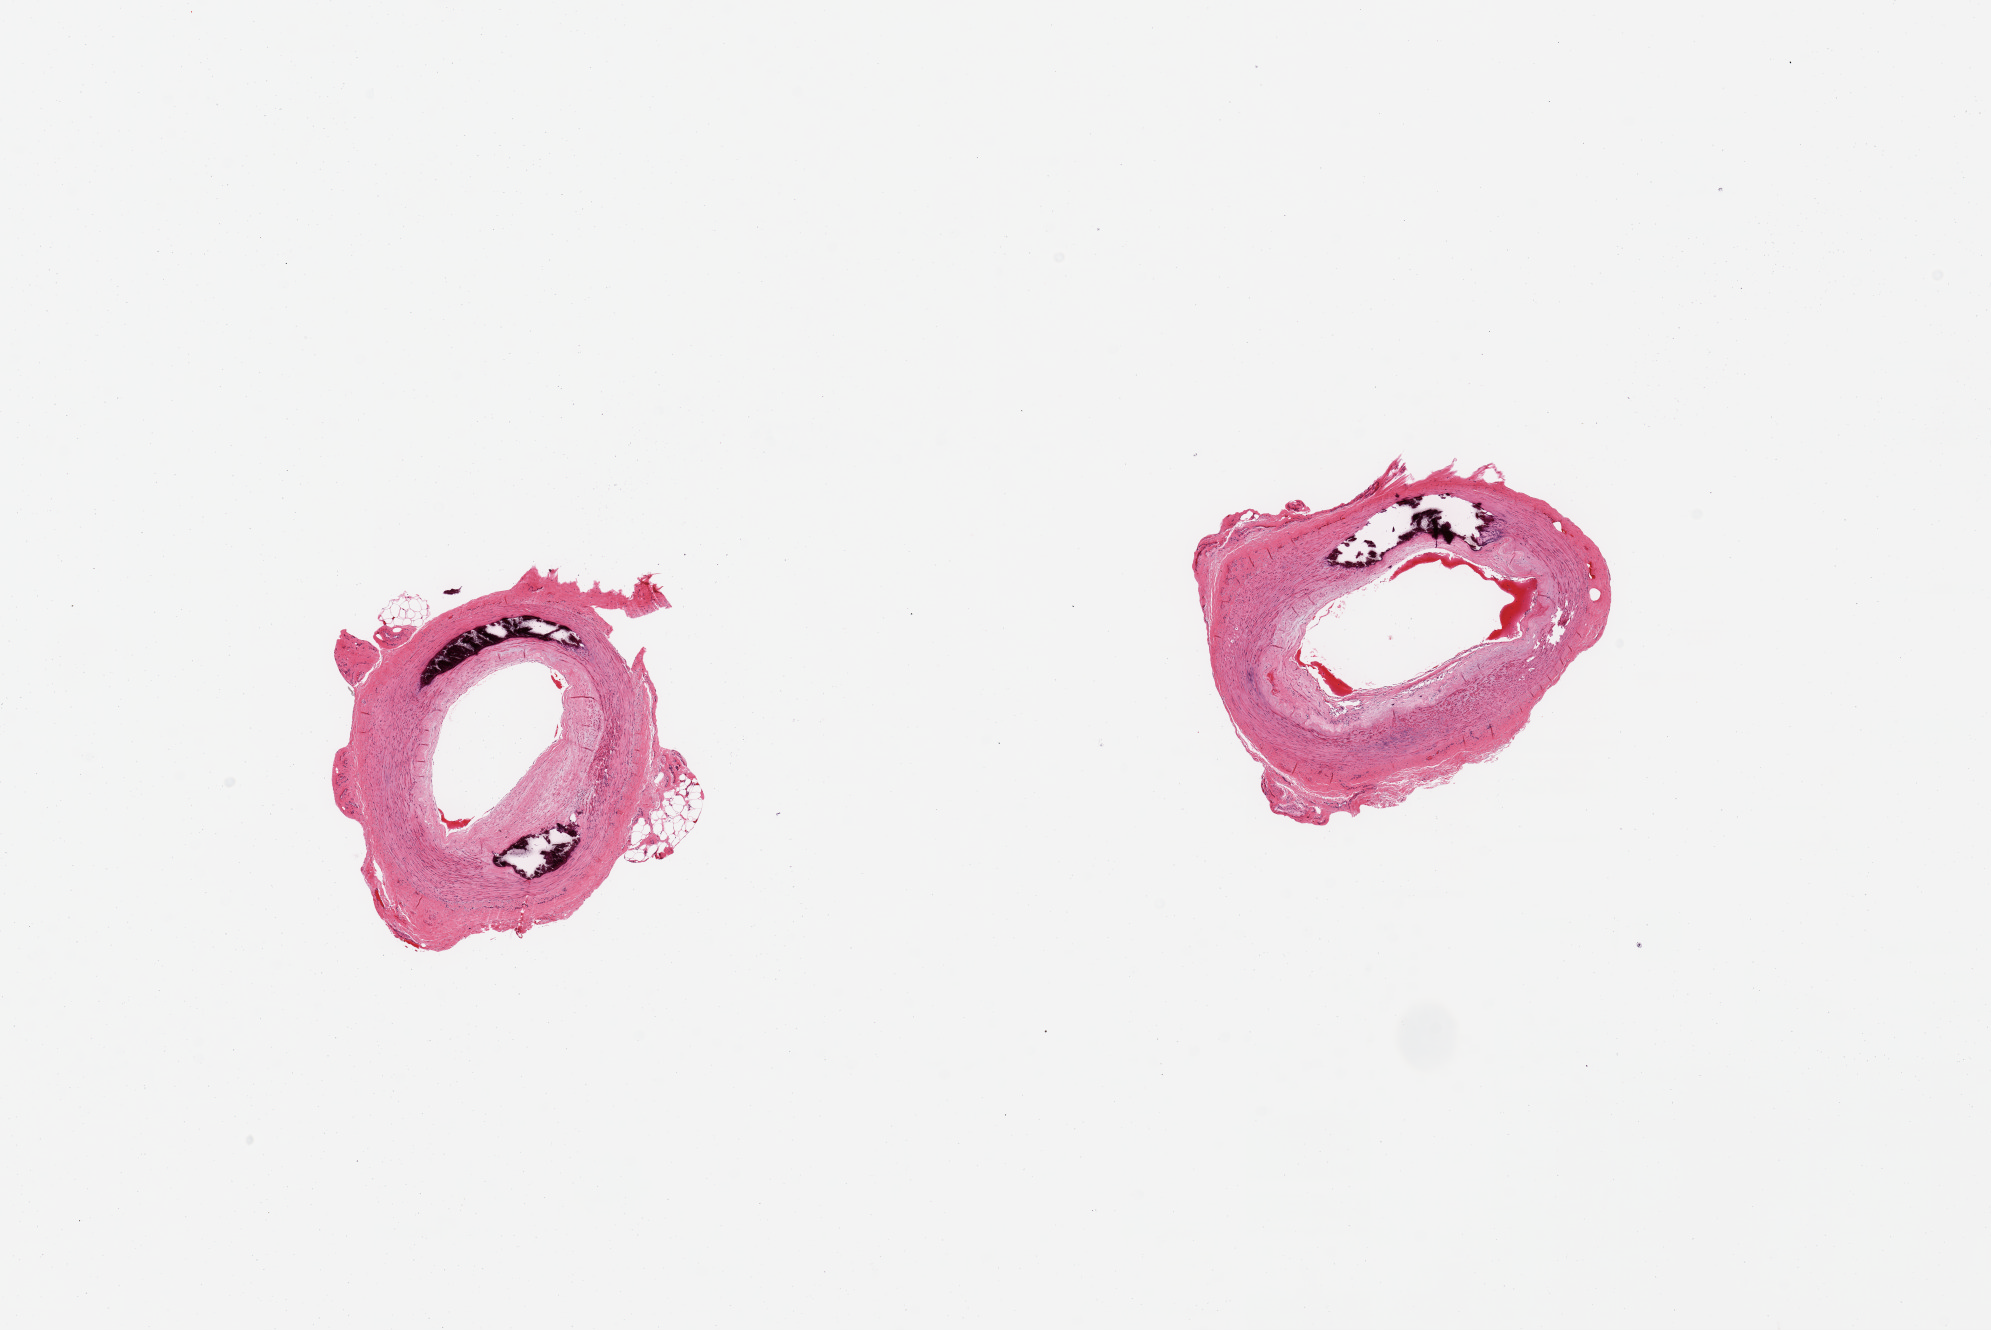
Whole-slide image, hematoxylin and eosin (H&E) stain — shown as a low-resolution overview of the whole scanned area (about 15.8 x 10.5 mm). PAXgene-fixed, paraffin-embedded tissue. Target tissue: tibial artery. Tissue donor sample.
Review note (as recorded): 2 pieces, no adherent fat; Monckeberg sclerosis; `20-30% occlusive atherosis.